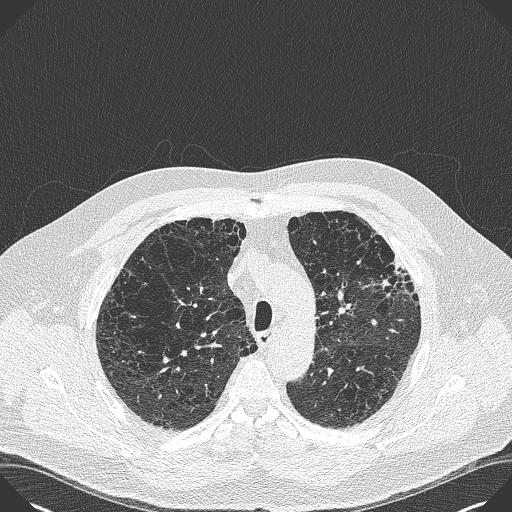
Axial slice from a low-dose chest CT screening exam; baseline screening round; lung window (W 1500 / L -600 HU); 1 mm slice thickness; lung (sharp) reconstruction kernel (B50f); slice 109 of 383 in the series. Male participant, aged 59 years at enrolment. Current smoker at enrolment.
Lesion marked by an expert reader, bounding box (x1, y1, x2, y2) in pixels: (372, 252, 429, 302). No non-calcified nodule or mass ≥4 mm was recorded by the screening reader at this exam. Official screen result: negative screen, minor abnormalities not suspicious for lung cancer. Participant outcome: lung cancer diagnosed 909 days after this screen (after the third annual screen) — bronchiolo-alveolar carcinoma, mixed mucinous and non-mucinous, left upper lobe, stage IA (AJCC 6th edition), 20 mm at pathology.